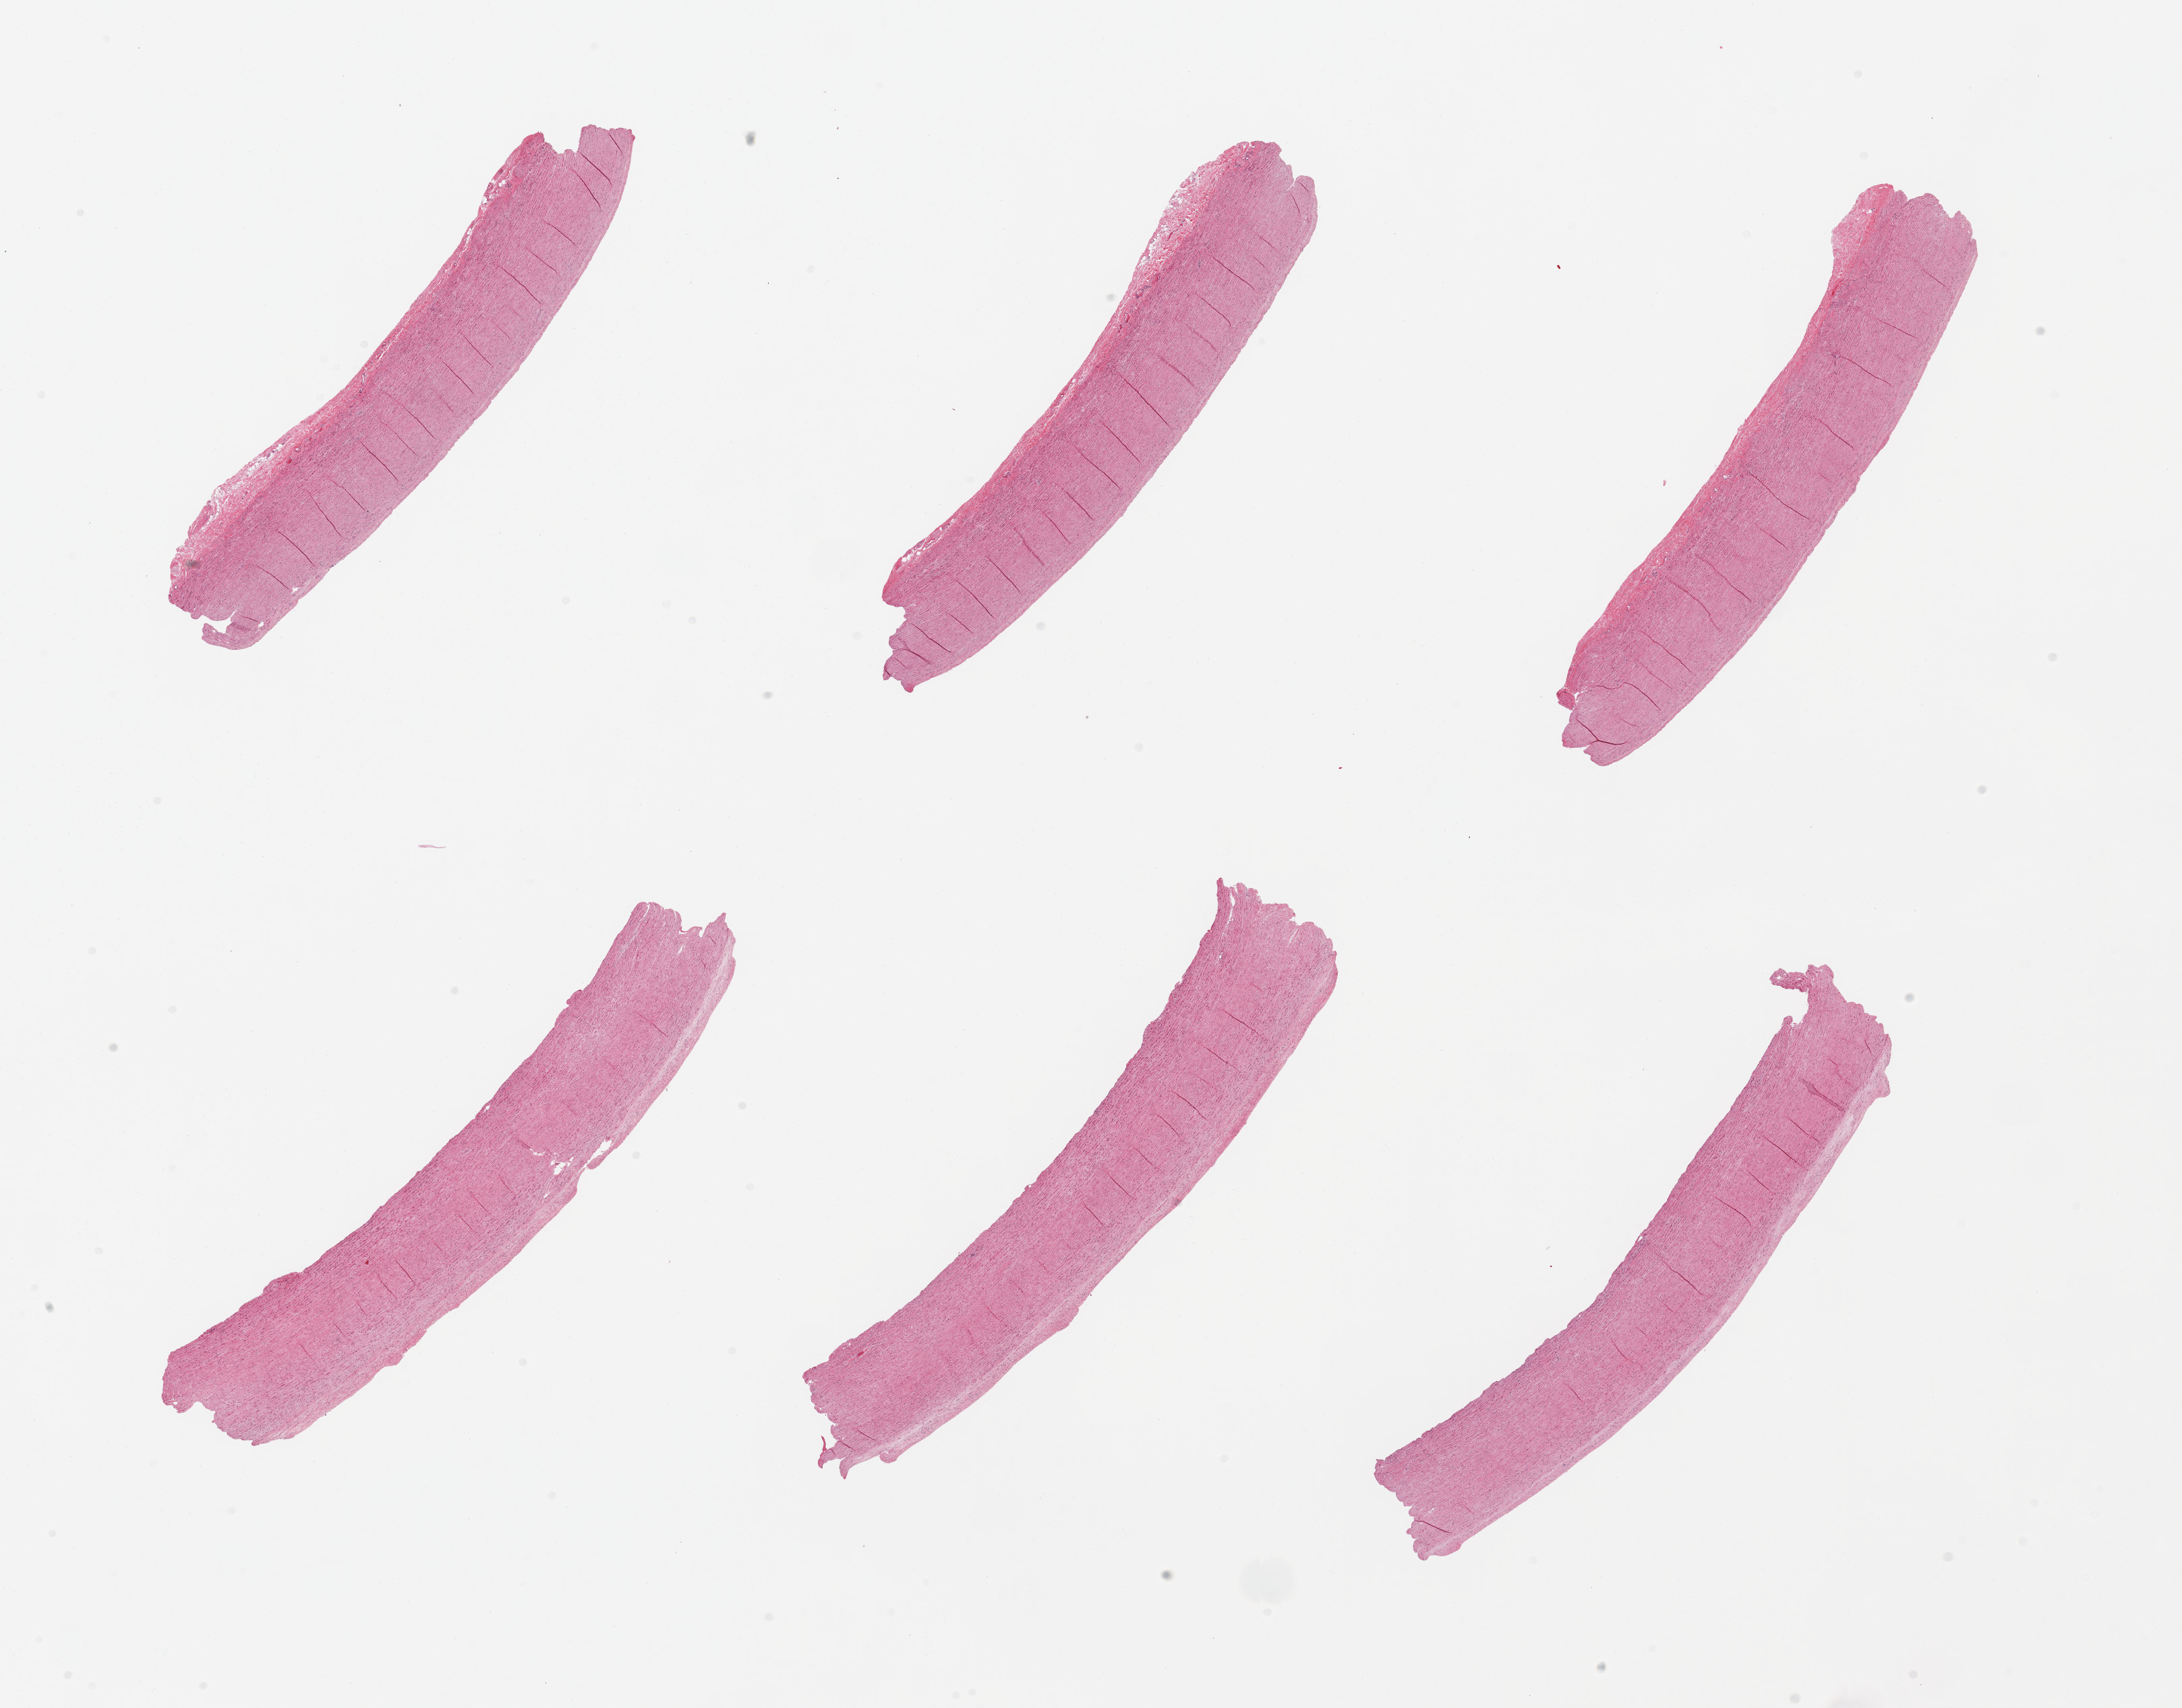
Digitized H&E-stained section — a low-resolution overview of the entire scanned area, about 25.6 x 20.0 mm (from a 20x scan). PAXgene-fixed, paraffin-embedded tissue. Section of aorta (target tissue). Tissue donor sample. Male donor.
Reviewer comment on this tissue sample: 6 pieces, atherosis up to ~0.2mm.